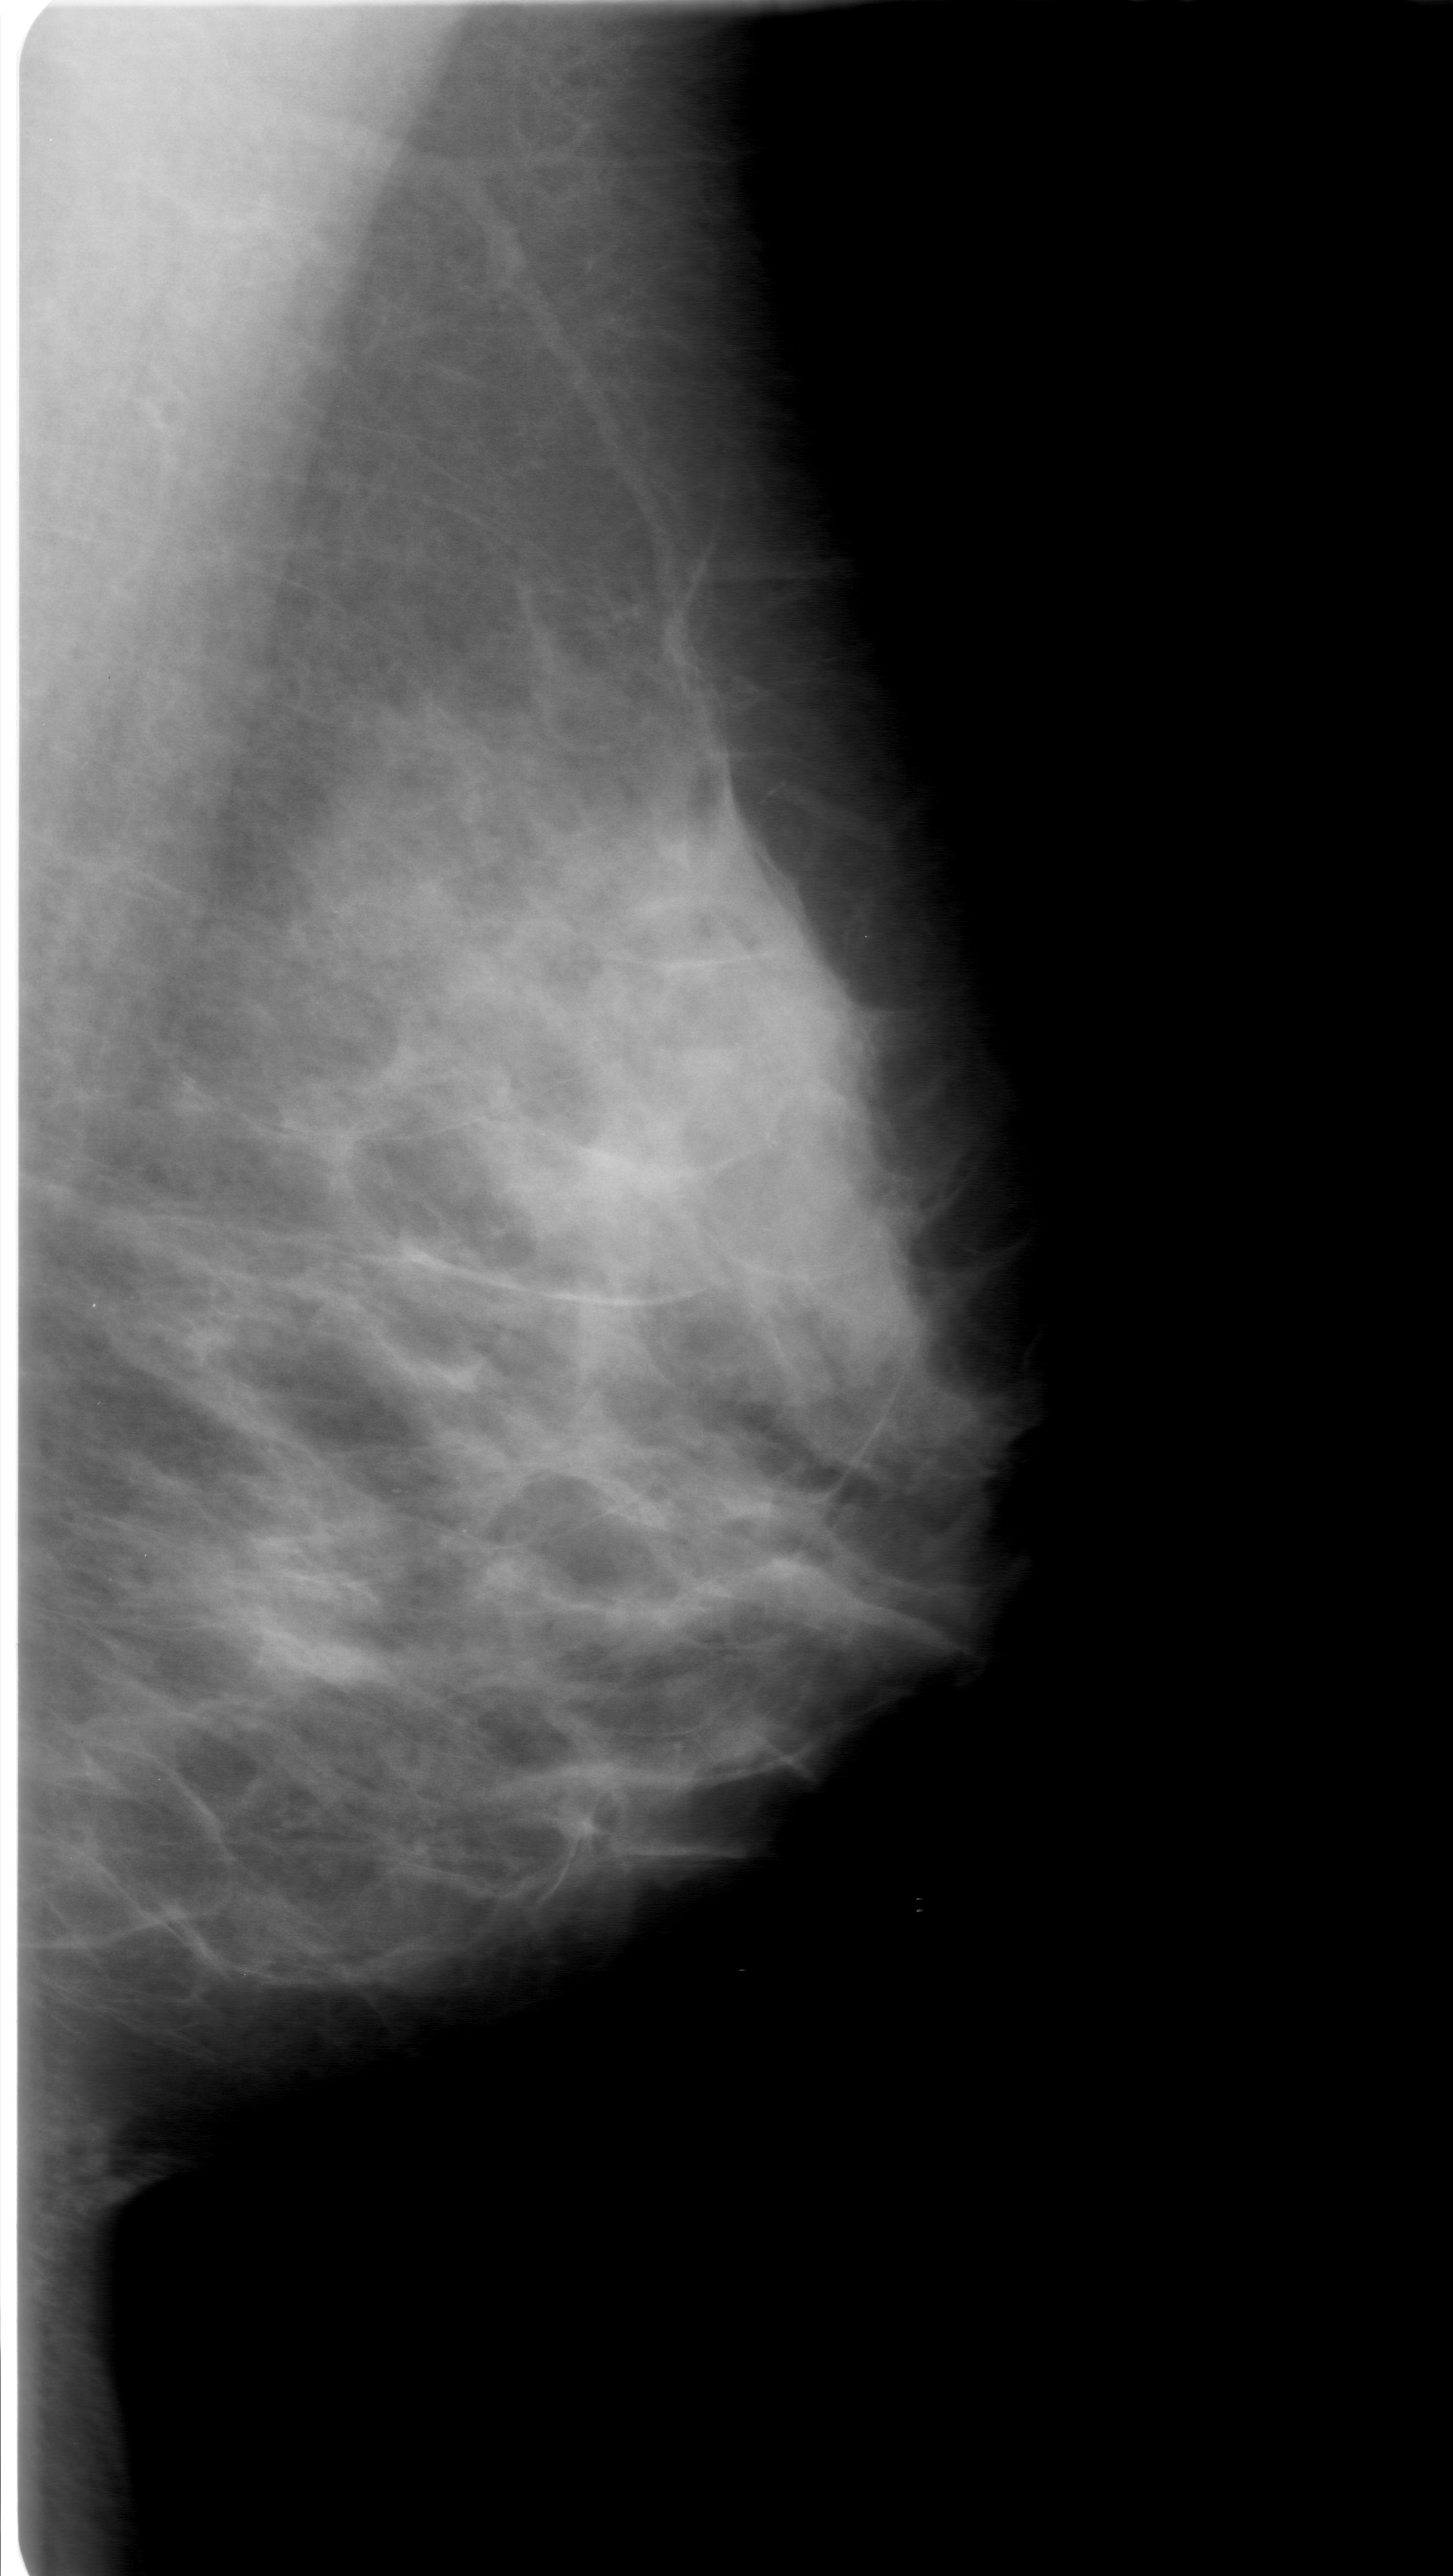
Mammogram (digitized film); left breast; MLO view; BI-RADS breast density category 3 (scale 1–4).
Abnormality record for this image: calcifications, morphology amorphous, distribution segmental; BI-RADS assessment category 0 (incomplete: needs additional imaging); pathology result (as recorded, not read from the image): benign.